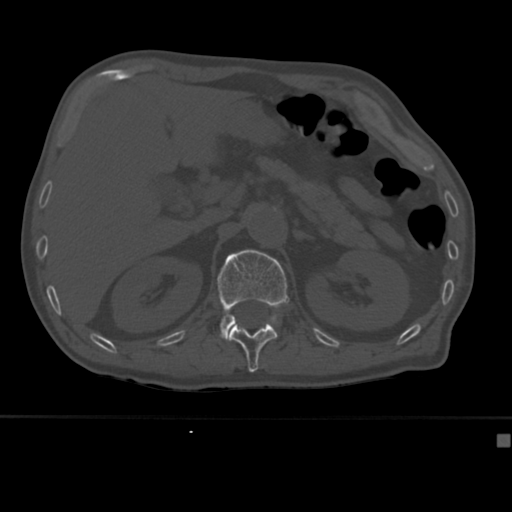
CT including the spine, one axial slice. Slice 179 of 430 in the series (ordered by position). 120 kVp. Bone window (W 1800 / L 400 HU). 1.5 mm slice thickness. 512 × 512 image matrix, field of view 337 × 337 mm. Male patient, age 64 years. Case-level facts recorded for this patient, not image findings: primary cancer: uterus.
Outlined on this slice (semi-automatic segmentation, software-assisted and operator-edited):
- L1 vertebra: bounding box [x1, y1, x2, y2] px = [217, 249, 289, 341]
- T12 vertebra: [229, 323, 278, 373]